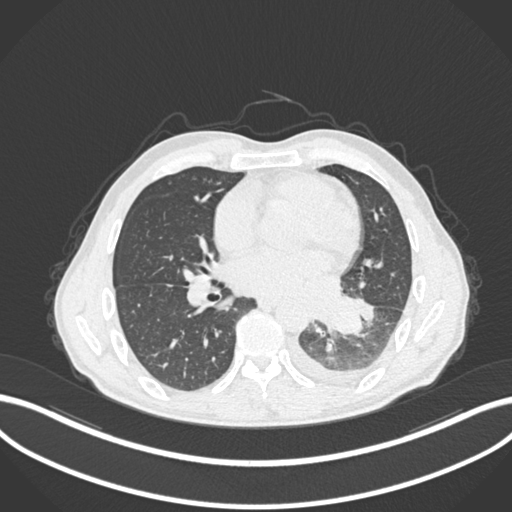
Chest CT, one axial slice. Slice 109 of 222 in the series (ordered by position). Reconstruction kernel B30f. Lung window (W 1500 / L -600 HU). 1 mm slice thickness. 512 × 512 image matrix. Patient: male, 47 years. From the clinical record (not read from this slice): clinical TNM (as recorded): T3 N1 M1c; histopathological grade: G3.
Structures marked on this image (bounding box drawn by a radiologist):
- lung tumour (recorded histology: small cell carcinoma): bounding box (x1, y1, x2, y2) in pixels: (313, 292, 363, 339)